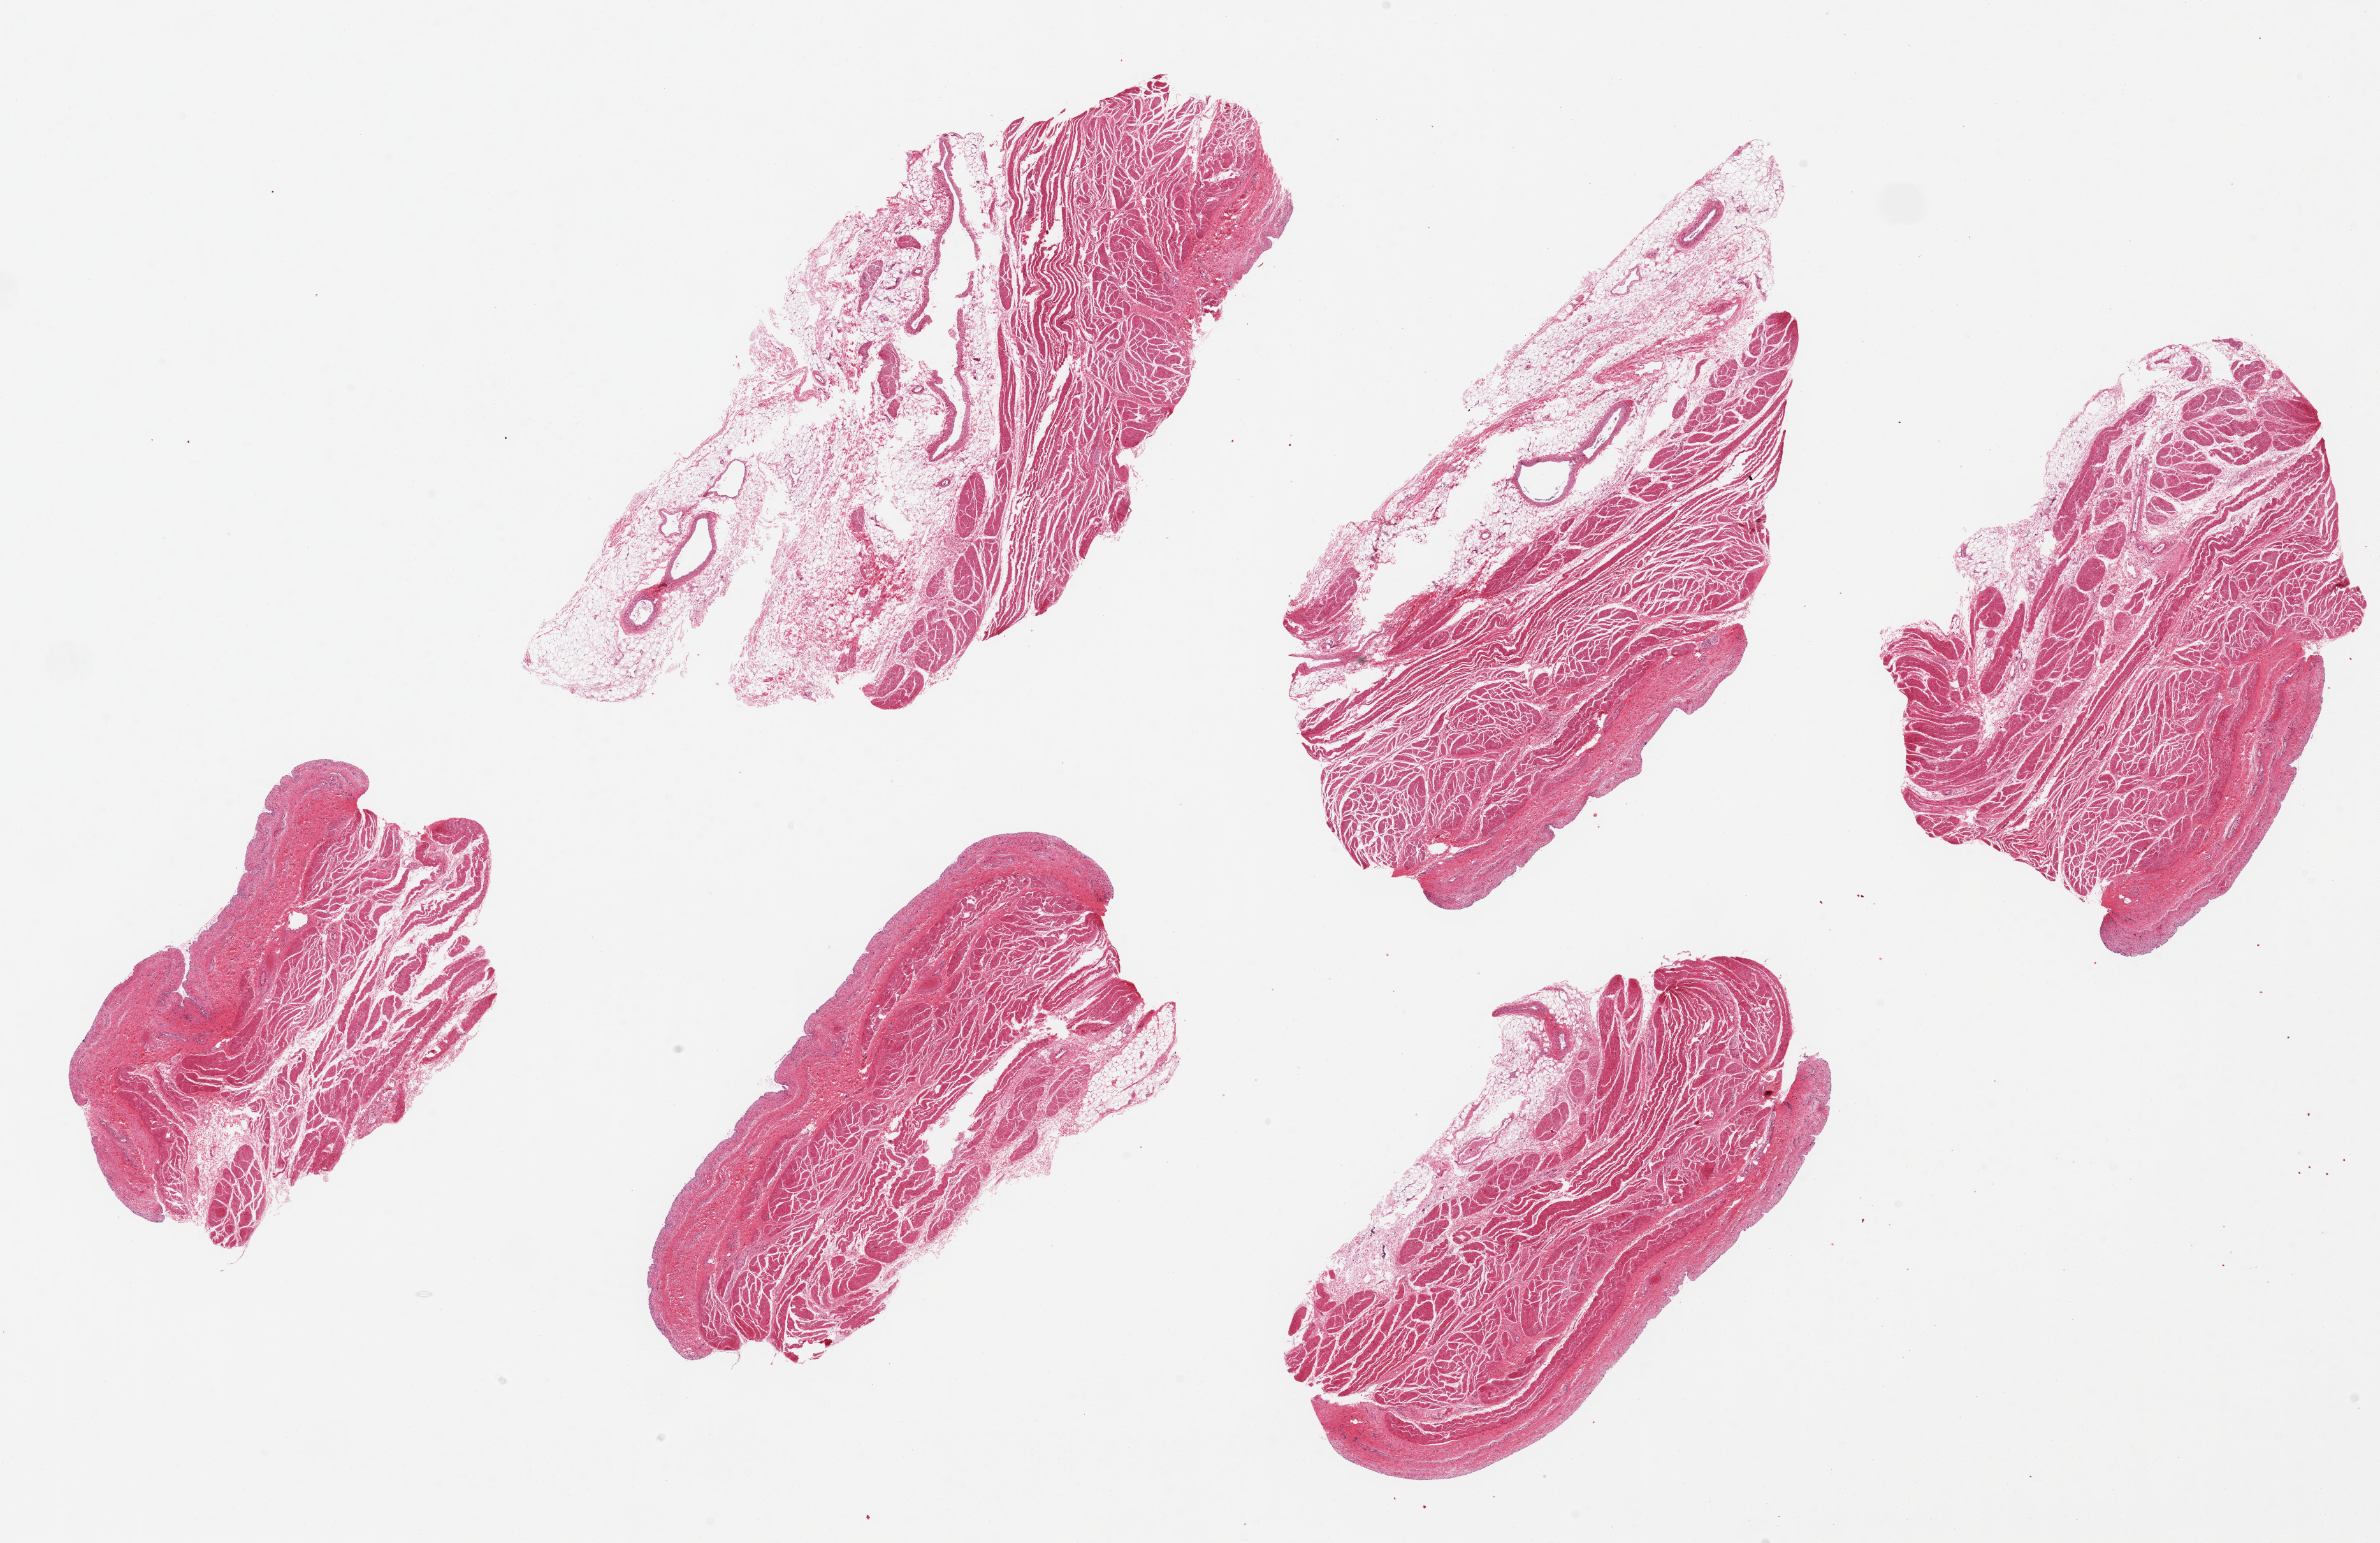
Digitized H&E-stained section — a low-resolution overview of the entire scanned area, about 29.5 x 19.1 mm (acquisition: 20x scan), PAXgene-fixed paraffin-embedded (PFPE) section, target tissue: urinary bladder, tissue donor sample. Male donor.
Reviewer comment on this tissue sample: 6 pieces up to 8.6x5 mm; epithelium totally sloughed; muscle wall in good shape.